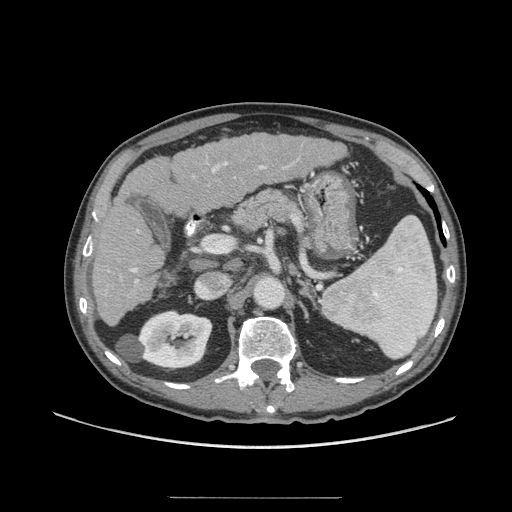
Contrast-enhanced abdominal CT (liver protocol), one axial slice. Slice 35 of 71 in the series (ordered by position). 140 kVp. Soft-tissue window (W 400 / L 40 HU). 512 × 512 image matrix. Case-level facts recorded for this patient, not image findings: diagnosis: hepatocellular carcinoma (patient treated with transarterial chemoembolisation; whether this scan precedes or follows treatment is not stated here); TNM stage (as recorded): Stage-I; Child-Pugh class: A; tumour differentiation: well differentiated; tumour nodularity: uninodular.
Annotated regions visible in this slice (semi-automatically segmented with operator editing):
- liver parenchyma outside the tumour (the mass and vessels are separate outlines, so this box may not span the whole liver): bounding box <92,132,346,326> (left, top, right, bottom; pixels)
- liver vessels: <130,162,267,284>